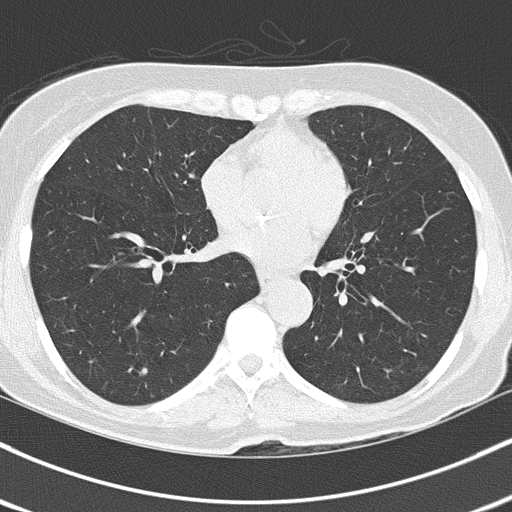
Chest CT (low-dose screening protocol), one axial image; baseline annual screen; lung window (W 1500 / L -600 HU); 2 mm slice thickness; lung (sharp) reconstruction kernel (B50f); 512 × 512 image matrix. Female, age 67 years at enrolment. Current smoker at enrolment.
Lesion marked by an expert reader, bounding box [x1, y1, x2, y2] px = [125, 358, 166, 388]. The exam's reader record, not a measurement of the box and not confirmed to be the same lesion: non-calcified nodule or mass ≥4 mm, left lower lobe, 7 × 6 mm, poorly defined margins, mixed attenuation. Note: the box lies in the patient's right hemithorax on this image, whereas the reader's record names the left lung; they may be different findings. Official screen result: positive, change unspecified: nodule(s) >= 4 mm or enlarging nodule(s), mass(es), or other non-specific abnormalities suspicious for lung cancer. Participant outcome: lung cancer diagnosed 876 days after this screen — adenocarcinoma, NOS, left lower lobe, poorly differentiated (G3), stage IA (AJCC 6th edition), 25 mm at pathology.